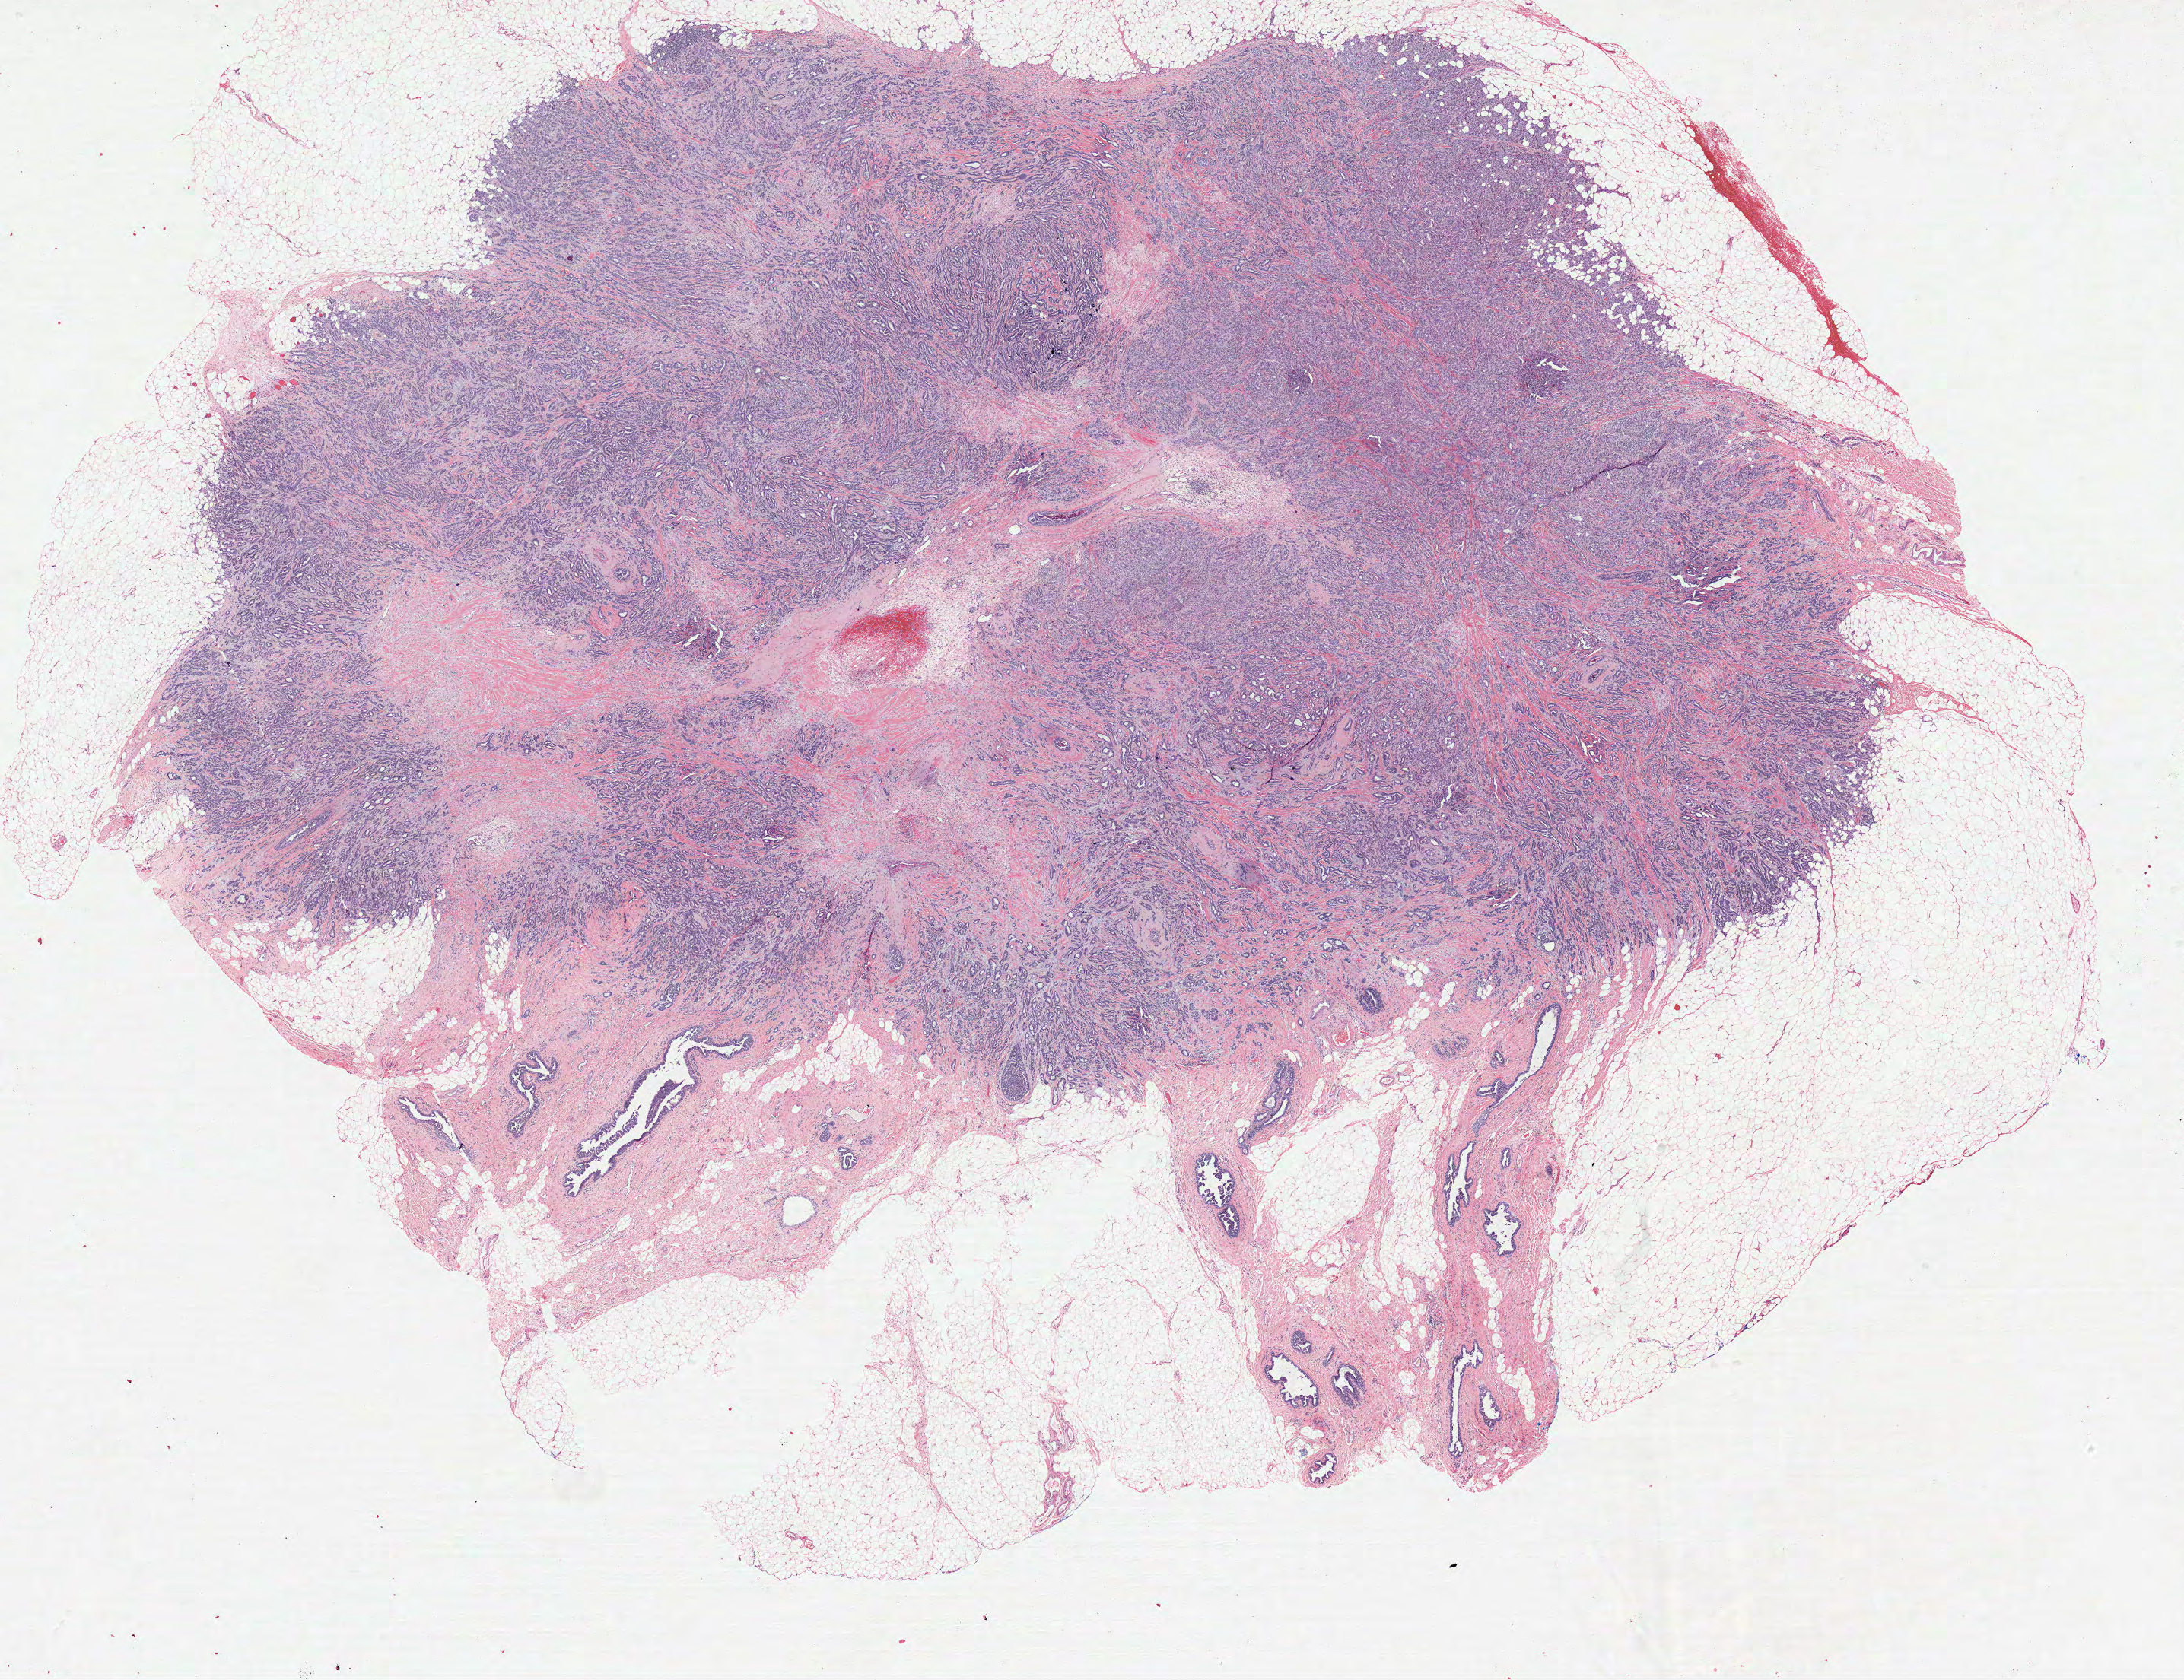
Whole-slide histology image, H&E — a low-resolution overview of the entire scanned area, about 22.9 x 17.6 mm (from a 20x scan), formalin-fixed paraffin-embedded (FFPE) diagnostic section, primary tumour sample from the breast. Female patient; age at initial diagnosis 77 years.
* histologic diagnosis: Infiltrating duct carcinoma, NOS
* laterality: left
* lymph nodes positive (case pathology): 0 of 9 examined
* AJCC pathologic stage: IIA (6th edition)
* TNM: T1 N1 M0